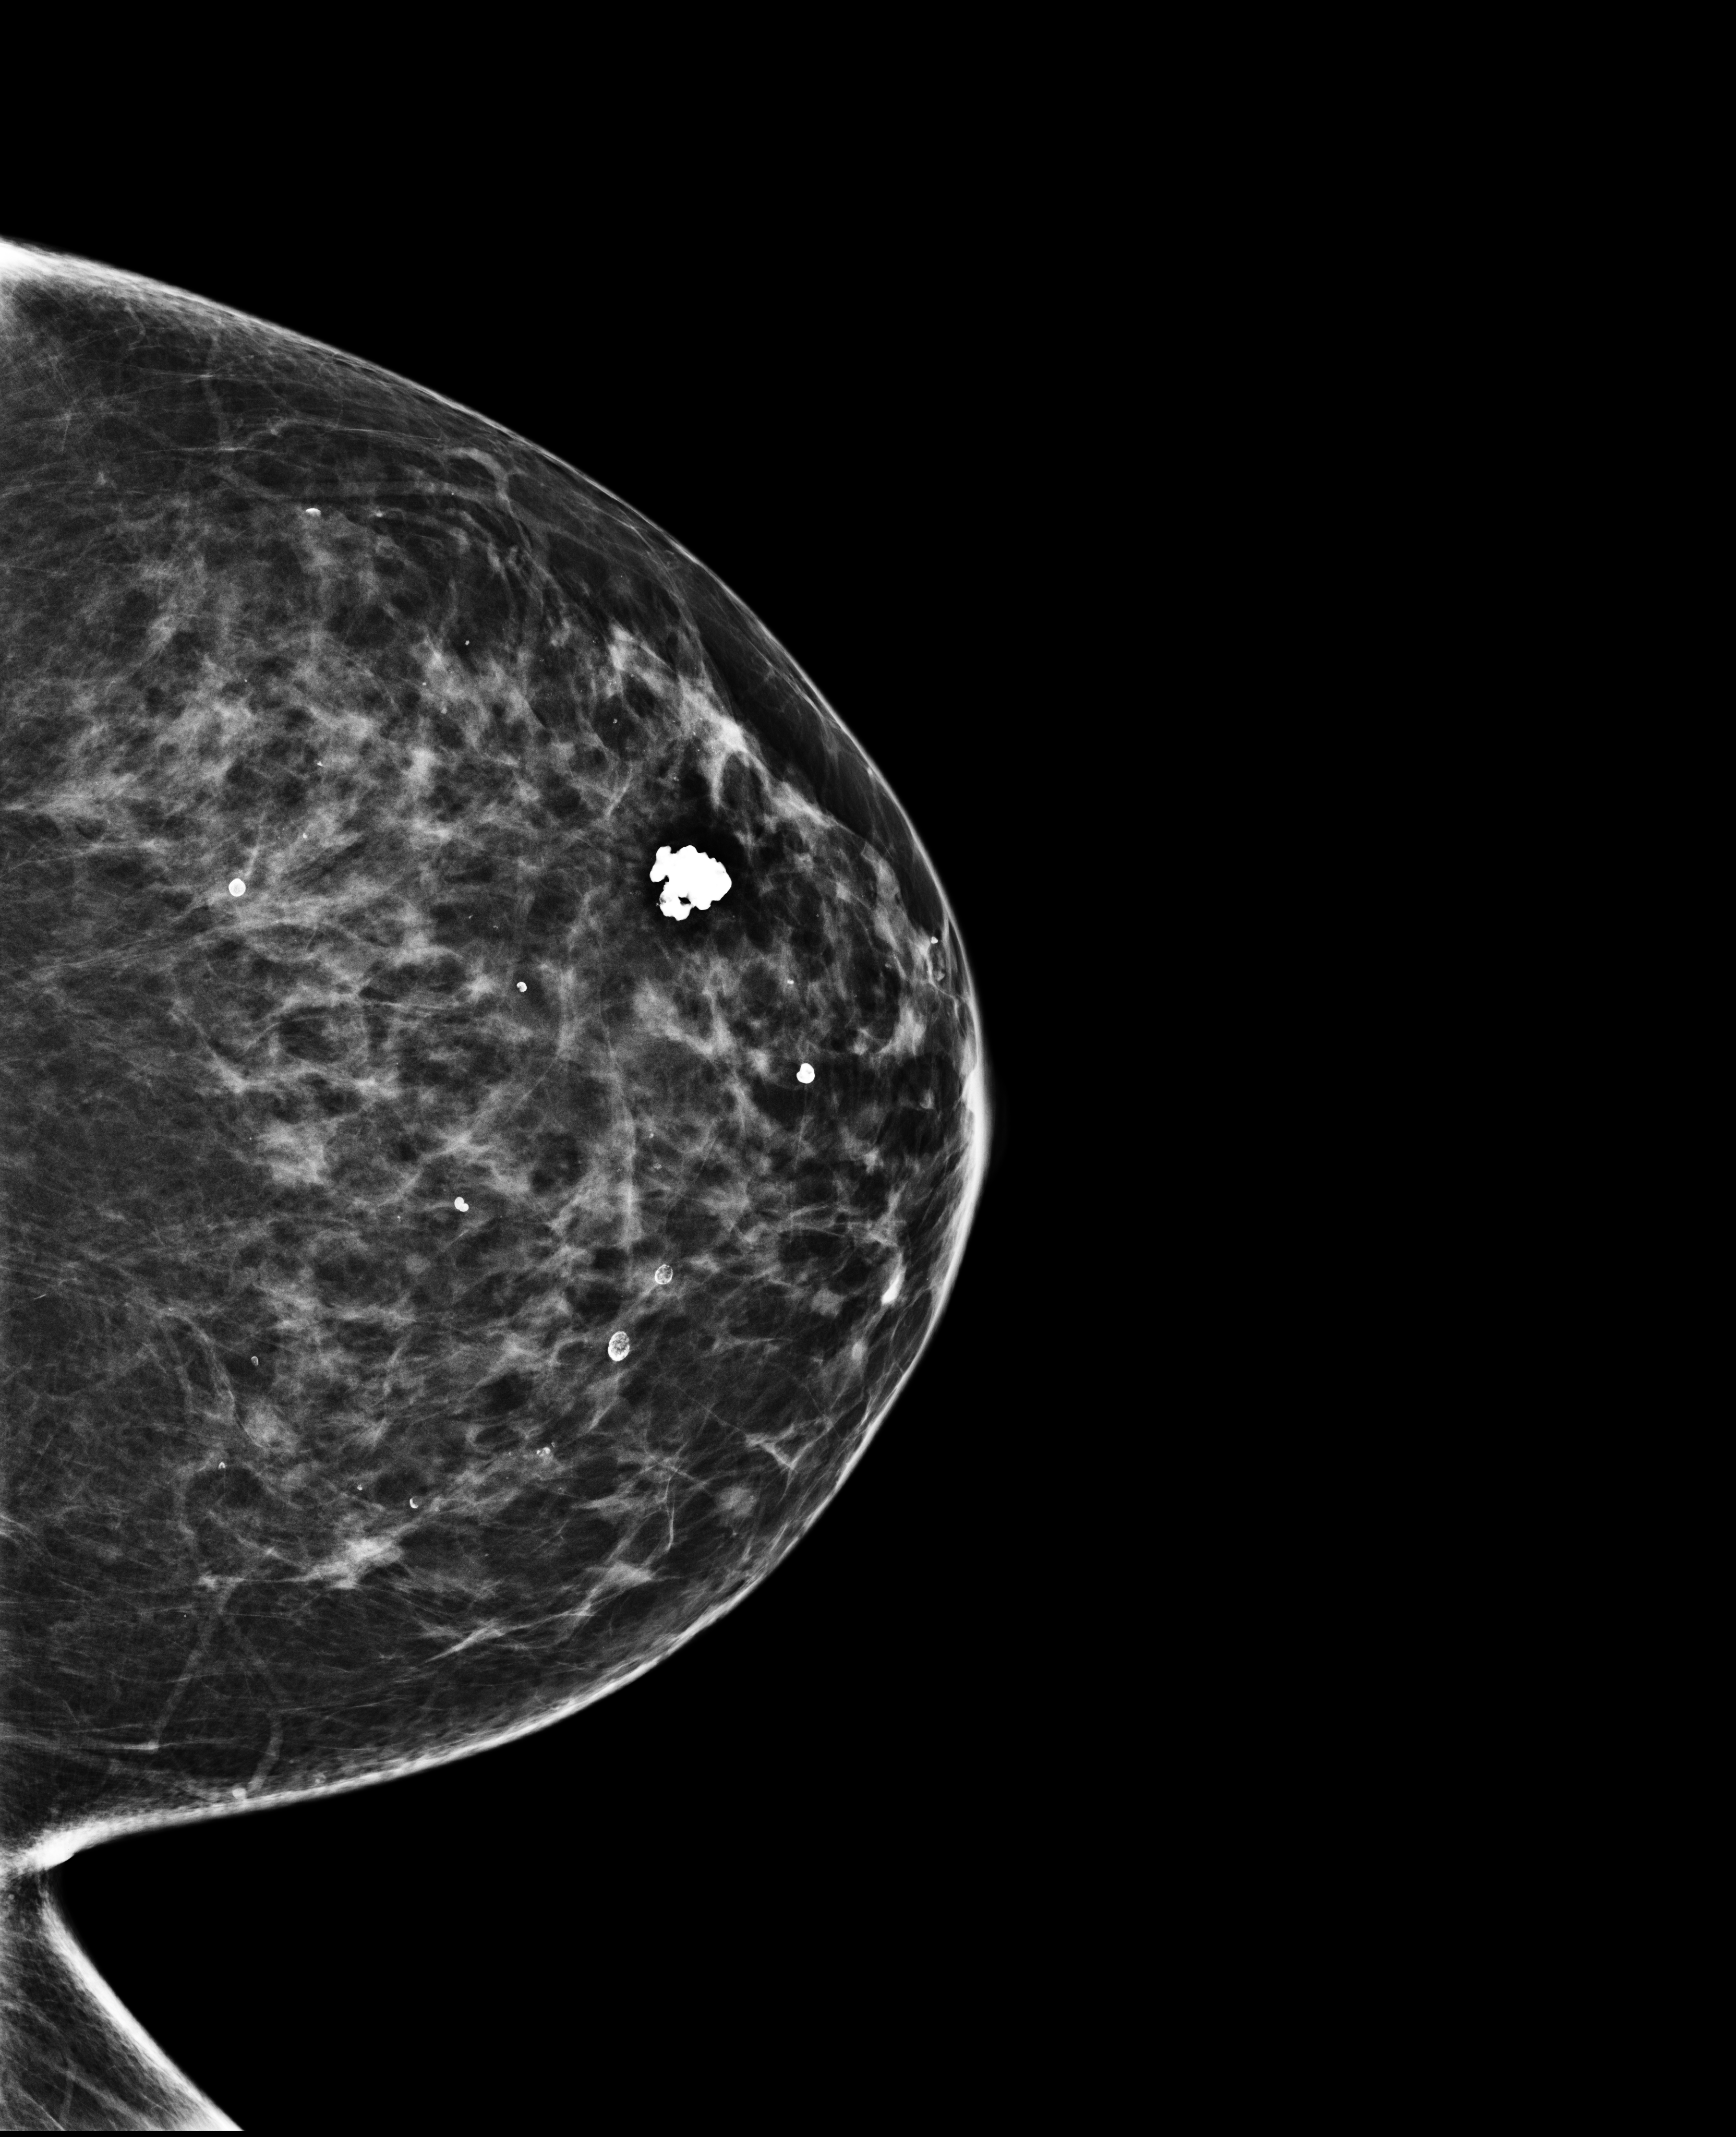
Annual screening mammography examination; system: Selenia Dimensions. Female patient, age 65 years.
Image type: full-field digital mammogram. Breast: left. Projection: craniocaudal (CC) view. Breast density at the screening exam (both breasts): heterogeneously dense (BI-RADS density category c). Final BI-RADS category for the screening round (tomosynthesis exam, both breasts): category 2. Recall: no recall after this screen.